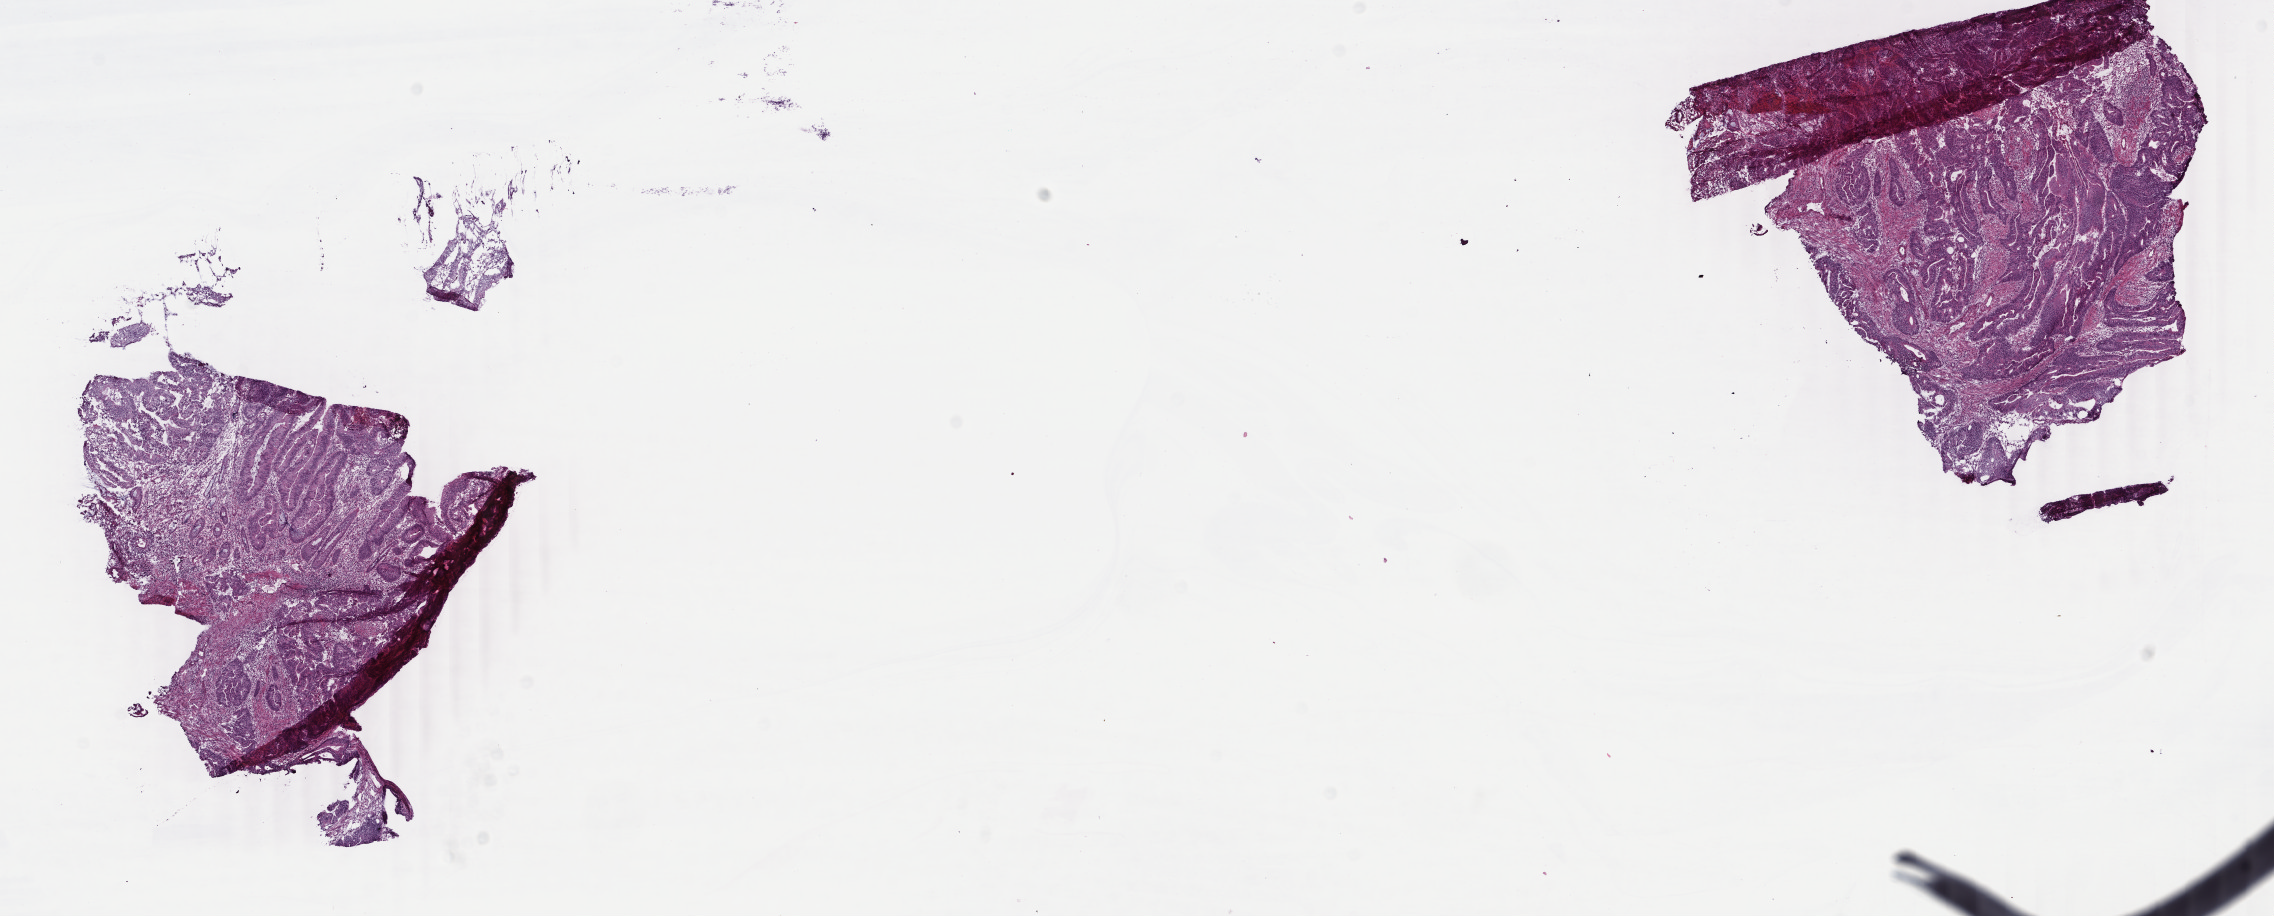
Hematoxylin and eosin (H&E) stained whole-slide image, shown as a low-resolution overview of the whole scanned area (about 18.1 x 7.3 mm); frozen section; primary tumour sample from the rectum. Patient: male, age at initial diagnosis 58 years. Slide review estimates, as recorded: tumour cells 85%, tumour nuclei 75%, normal cells 5%, stromal cells 8%, necrosis 2%. Inflammatory infiltration, as recorded: lymphocyte infiltration 15%, monocyte infiltration 3%, neutrophil infiltration 2%.
AJCC pathologic stage: IIIB (6th edition). Diagnosis: Adenocarcinoma, NOS.